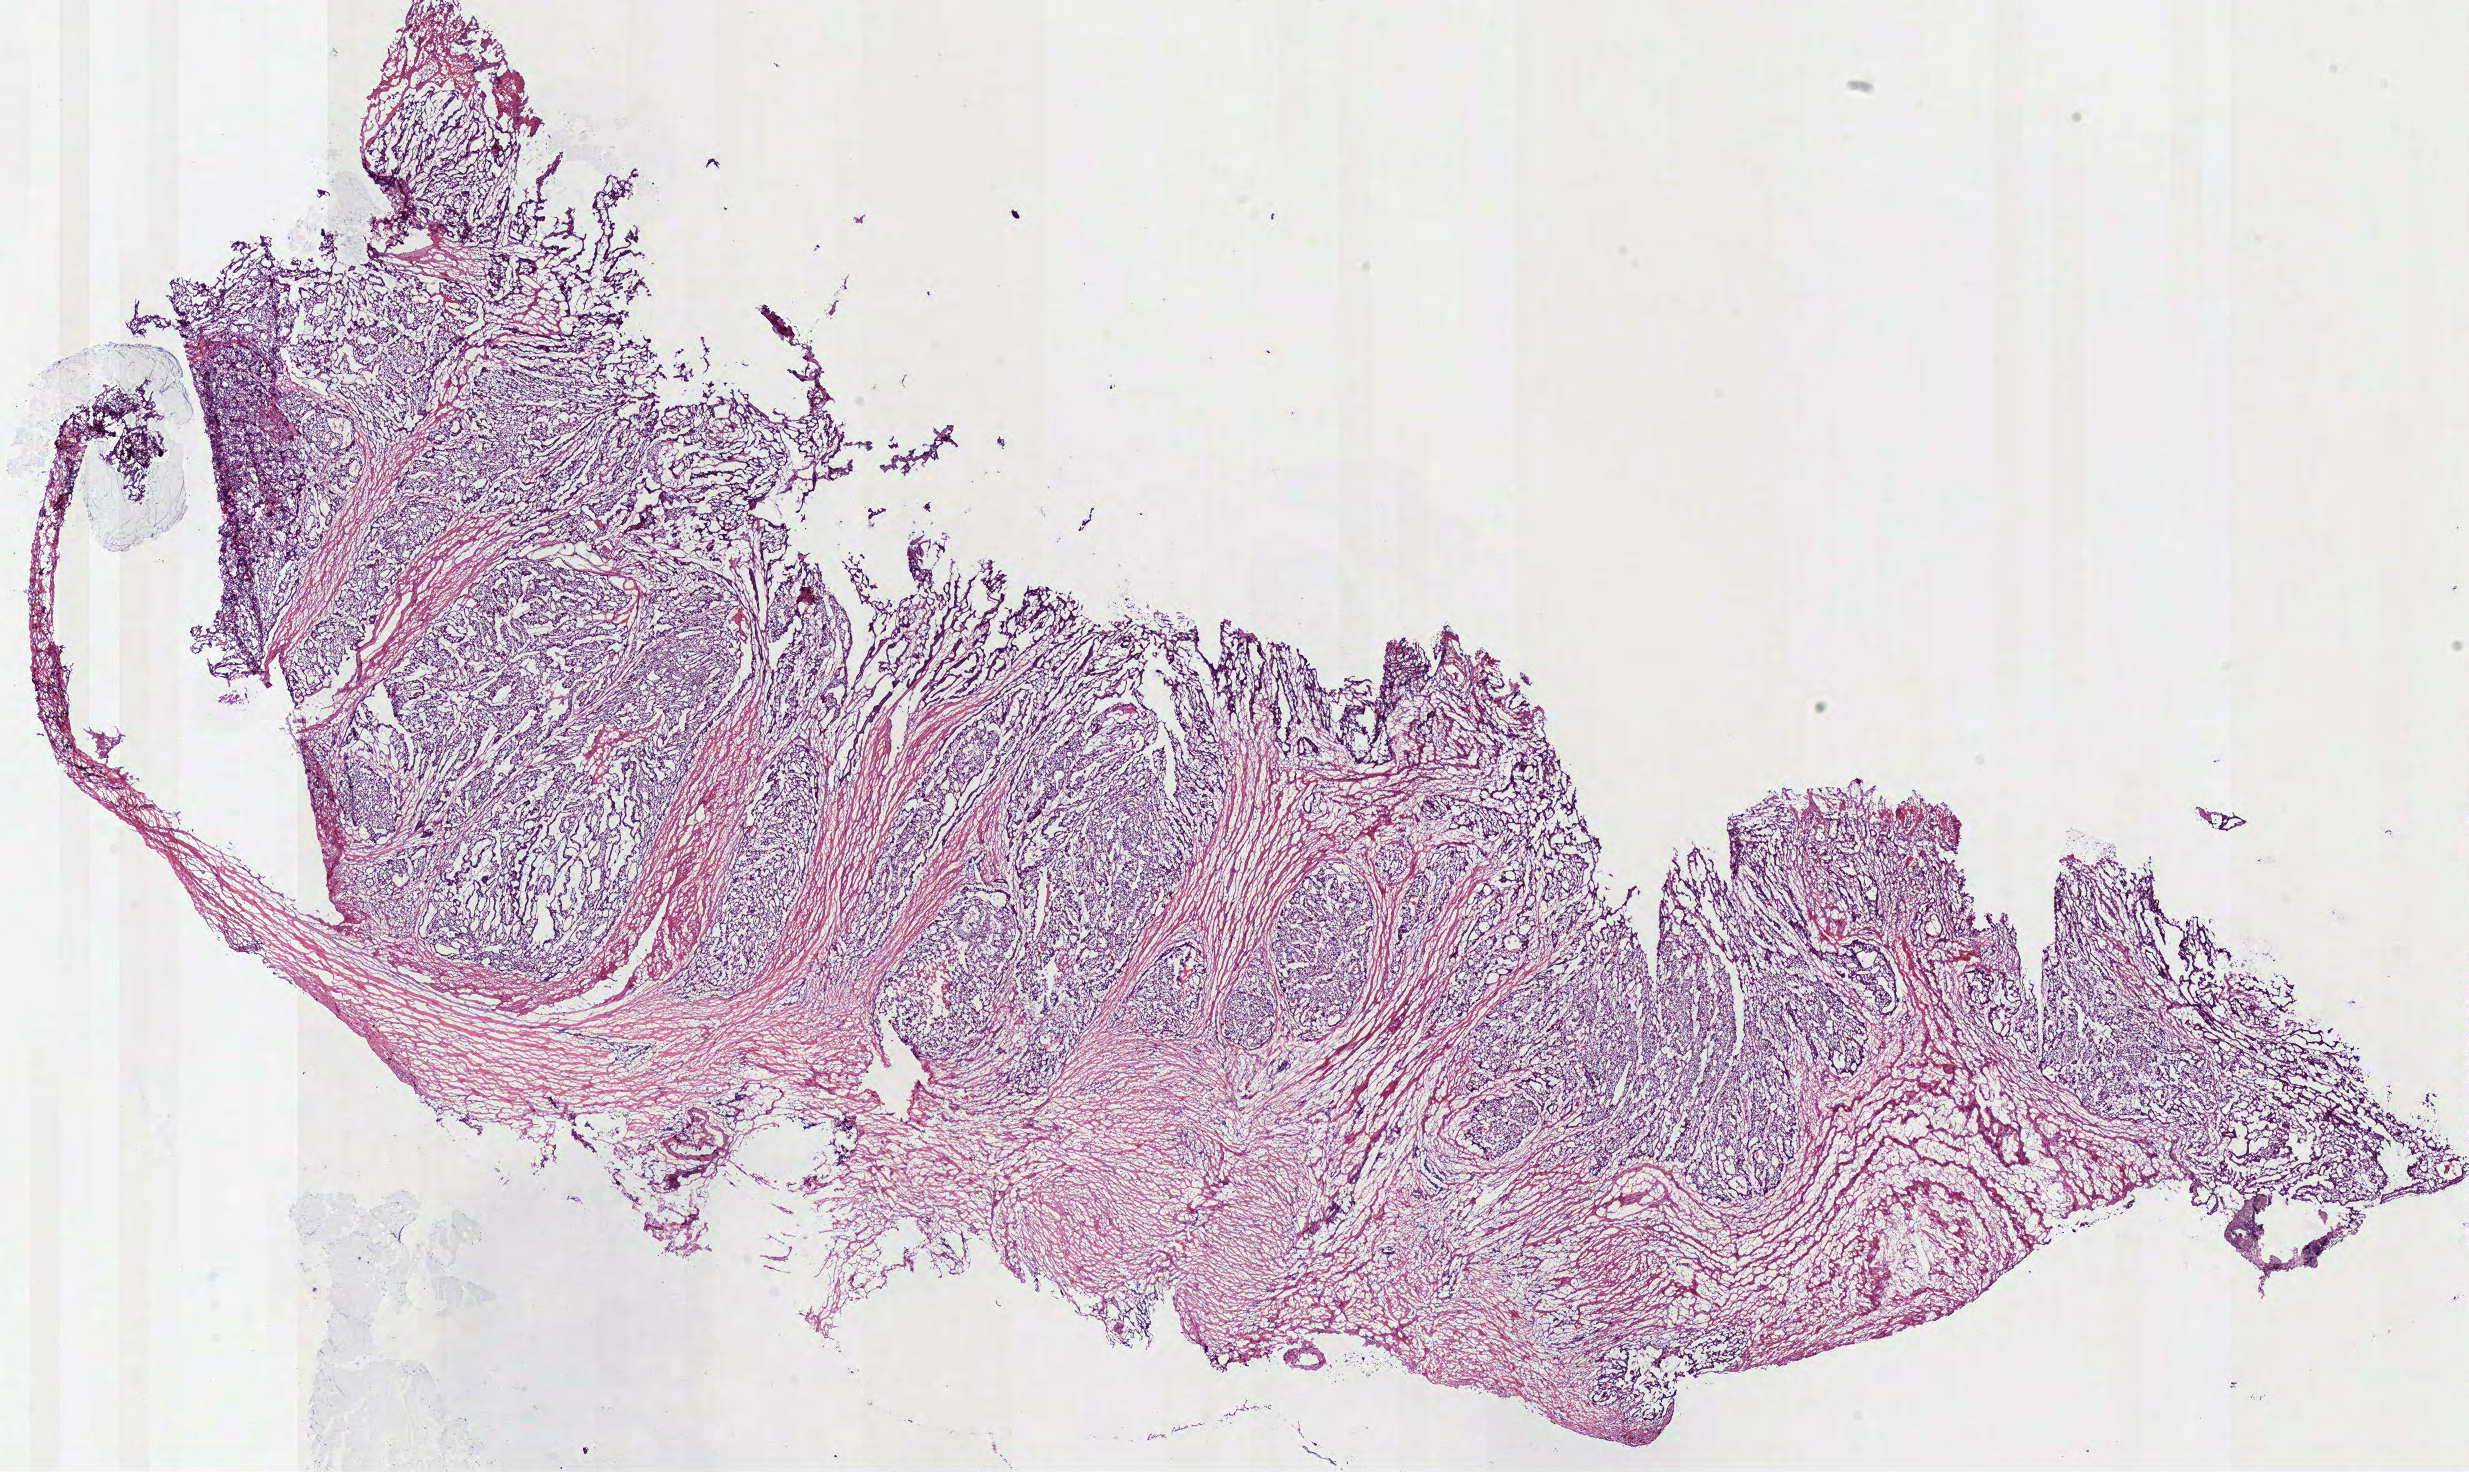
Whole-slide histology image, H&E — whole scanned area (about 19.5 x 11.6 mm) shown as a low-resolution overview; frozen section from the top of the tissue portion; primary tumour sample from the colon. Patient: female, age at initial diagnosis 77 years. Composition of this section per pathologist review: tumour cells 62%, tumour nuclei 80%, normal cells 0%, stromal cells 35%, necrosis 3%.
* lymph nodes positive (case pathology): 0 of 8 examined
* pathologic diagnosis: Adenocarcinoma, NOS
* AJCC pathologic stage: IIA (7th edition)